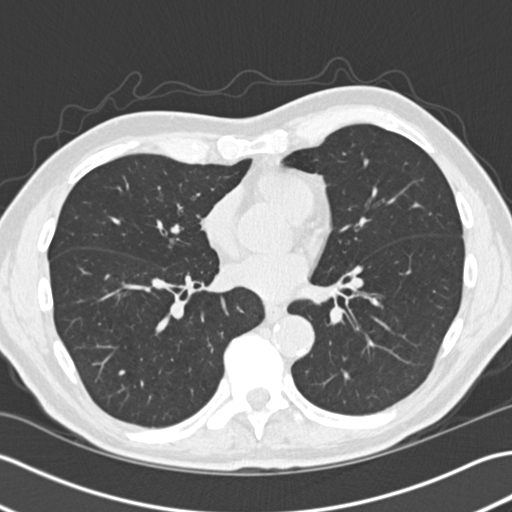
Low-dose screening chest CT, one axial slice. Slice 76 of 172 in the series (ordered by position). Lung window (W 1500 / L -600 HU). 2 mm slice thickness. 512 × 512 image matrix, field of view 350 × 350 mm.
Annotated regions visible in this slice (manually delineated by an expert):
- lesion 1 (tumor, lower lobe of right lung): bounding box <105,278,141,288> (left, top, right, bottom; pixels)